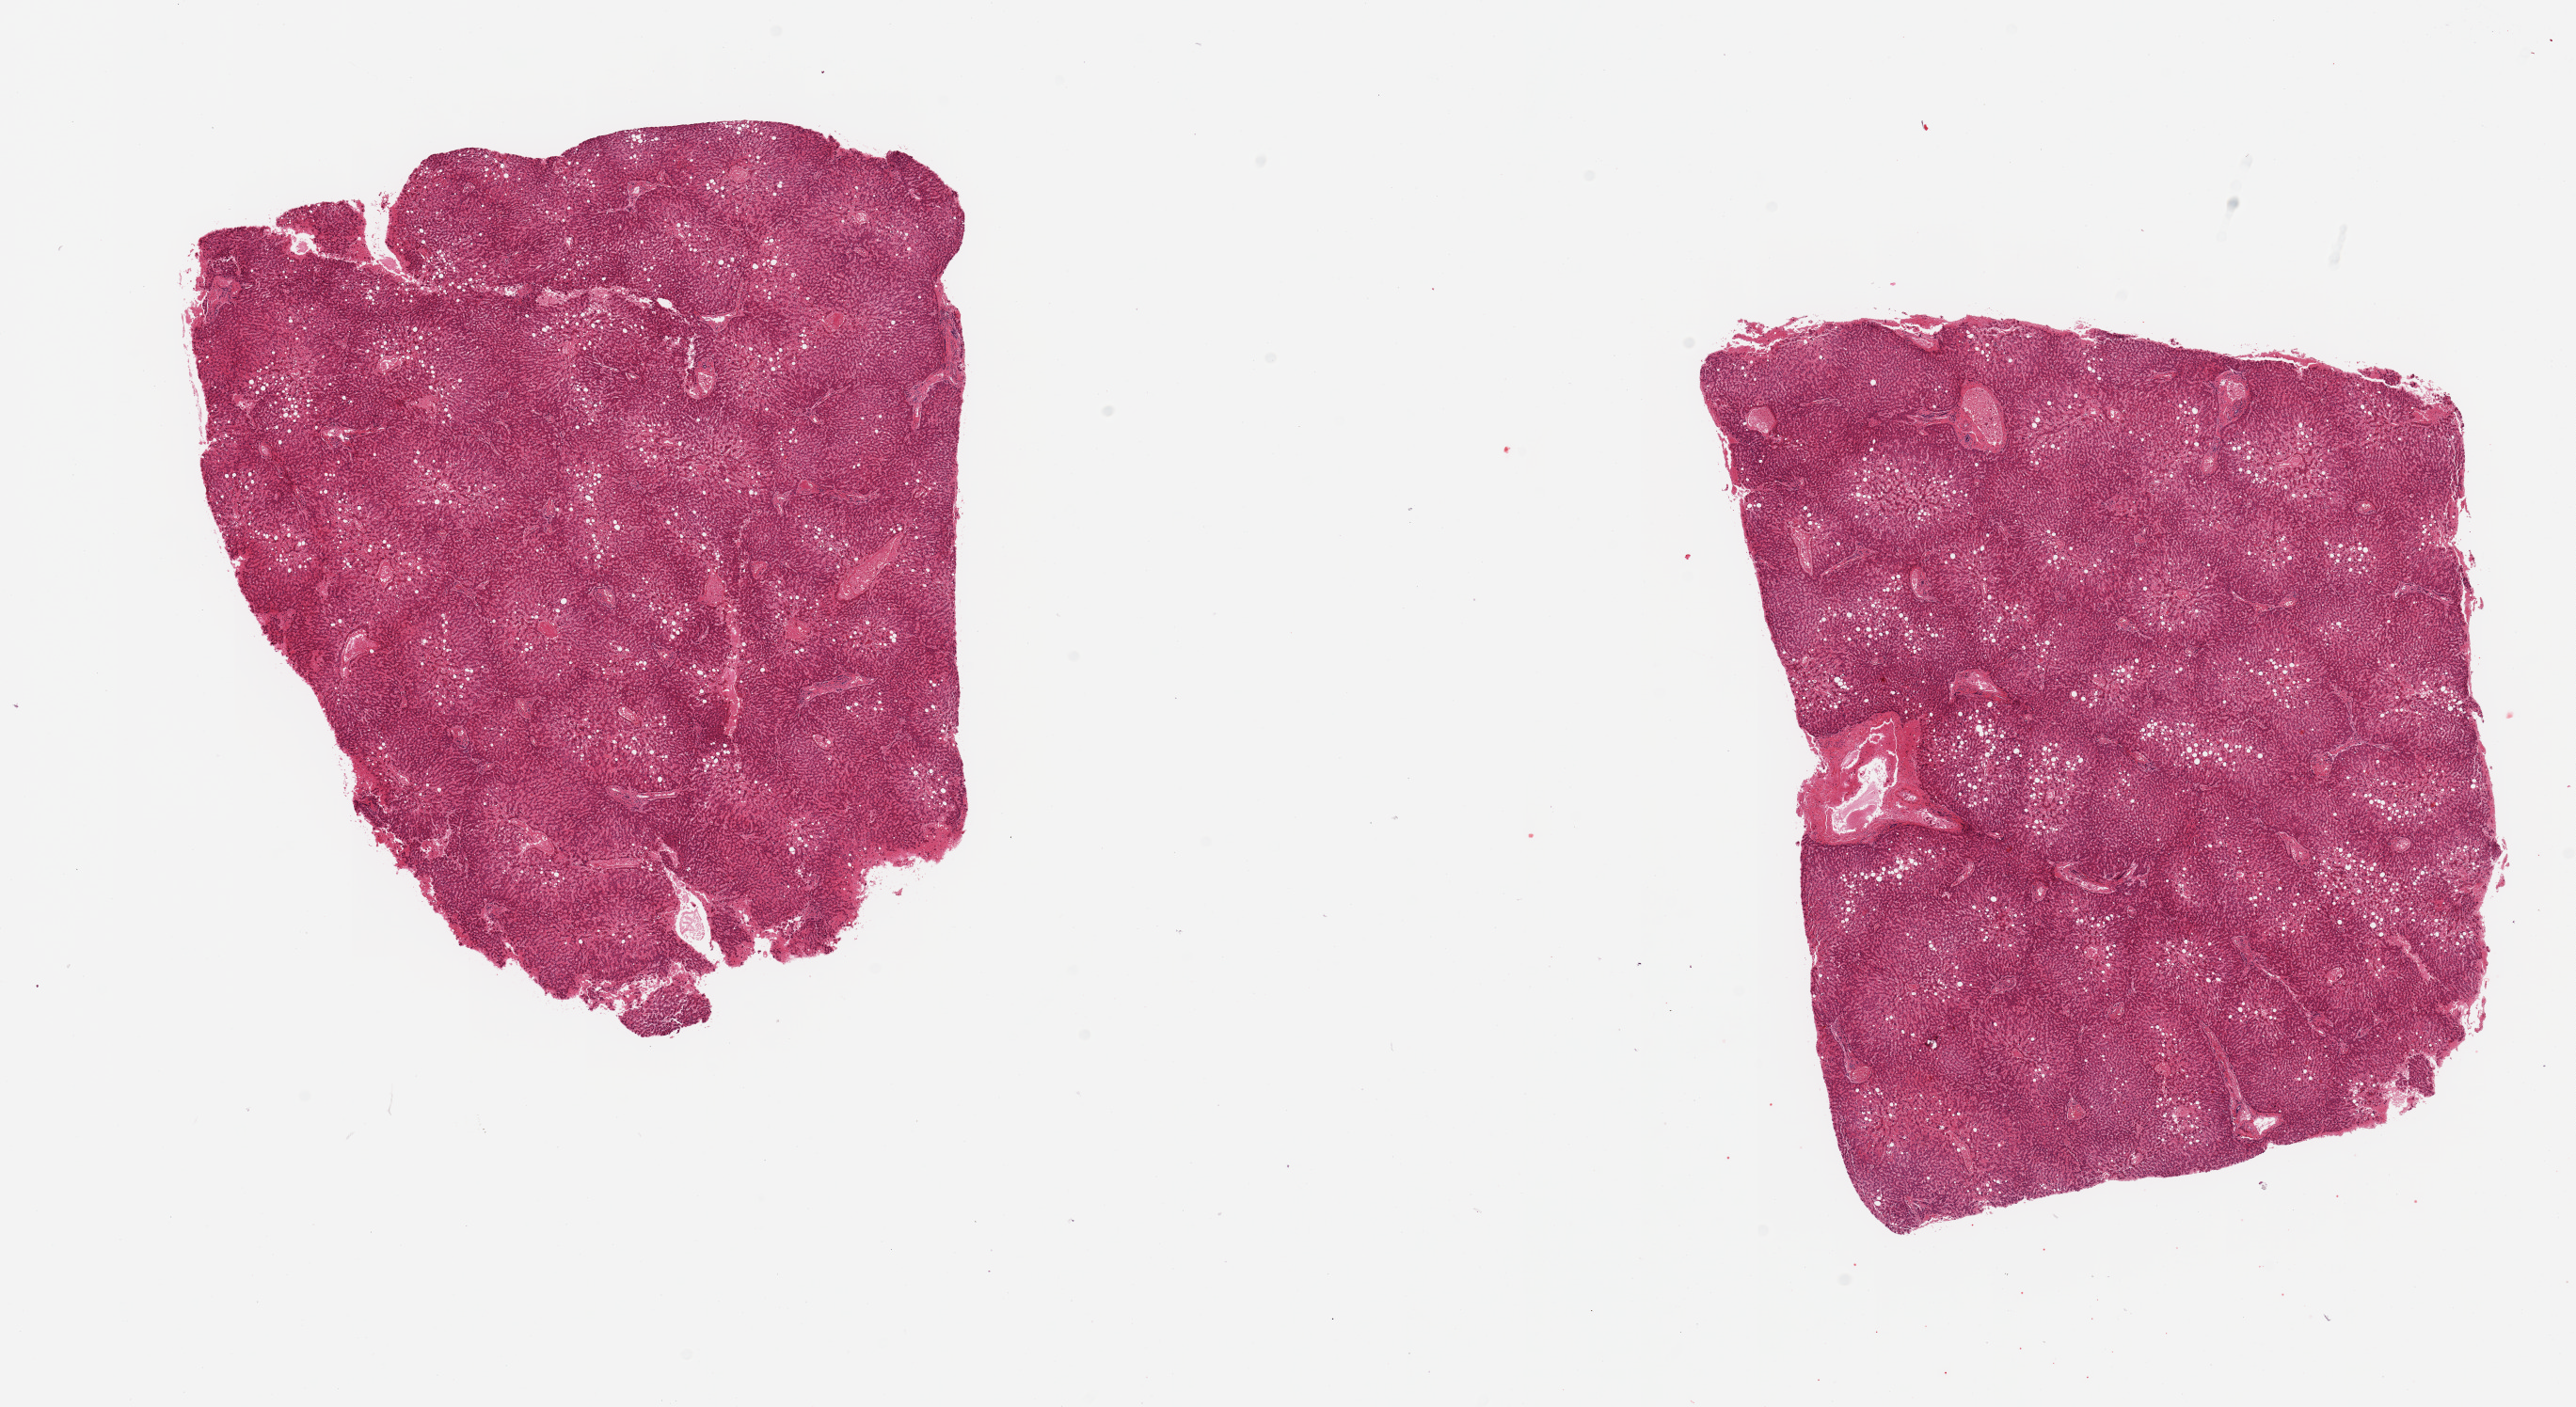
Digitized H&E-stained section, low-resolution overview of the scanned area, about 21.7 x 11.8 mm; PAXgene-fixed, paraffin-embedded tissue; section of liver (target tissue); tissue donor sample. Male donor.
Pathologist's review note for this sample: 2 pieces; moderate congestion and mild macrovesicular steatosis.